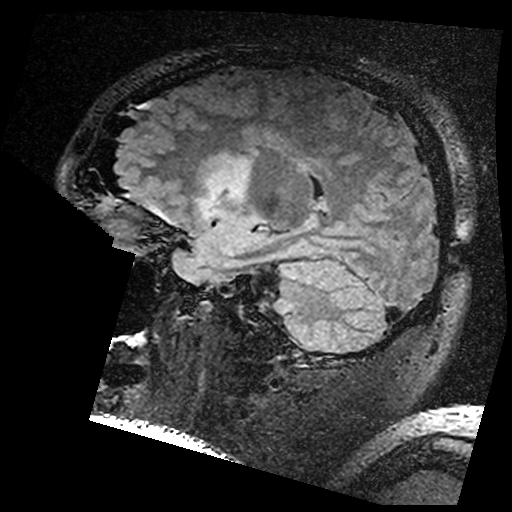
Brain MRI from a brain-tumour surgery series, one sagittal slice; position 111 of 176 along the scan axis; T2 FLAIR; 512 × 512 image matrix, field of view 250 × 250 mm. Case-level facts recorded for this patient, not image findings: histopathology: Astrocytoma; WHO grade: 3; IDH mutation: yes; tumour location: Left Insular.
Annotated regions visible in this slice (outlined manually by an expert reader):
- residual tumour: bounding box [x1, y1, x2, y2] px = [206, 149, 251, 202]